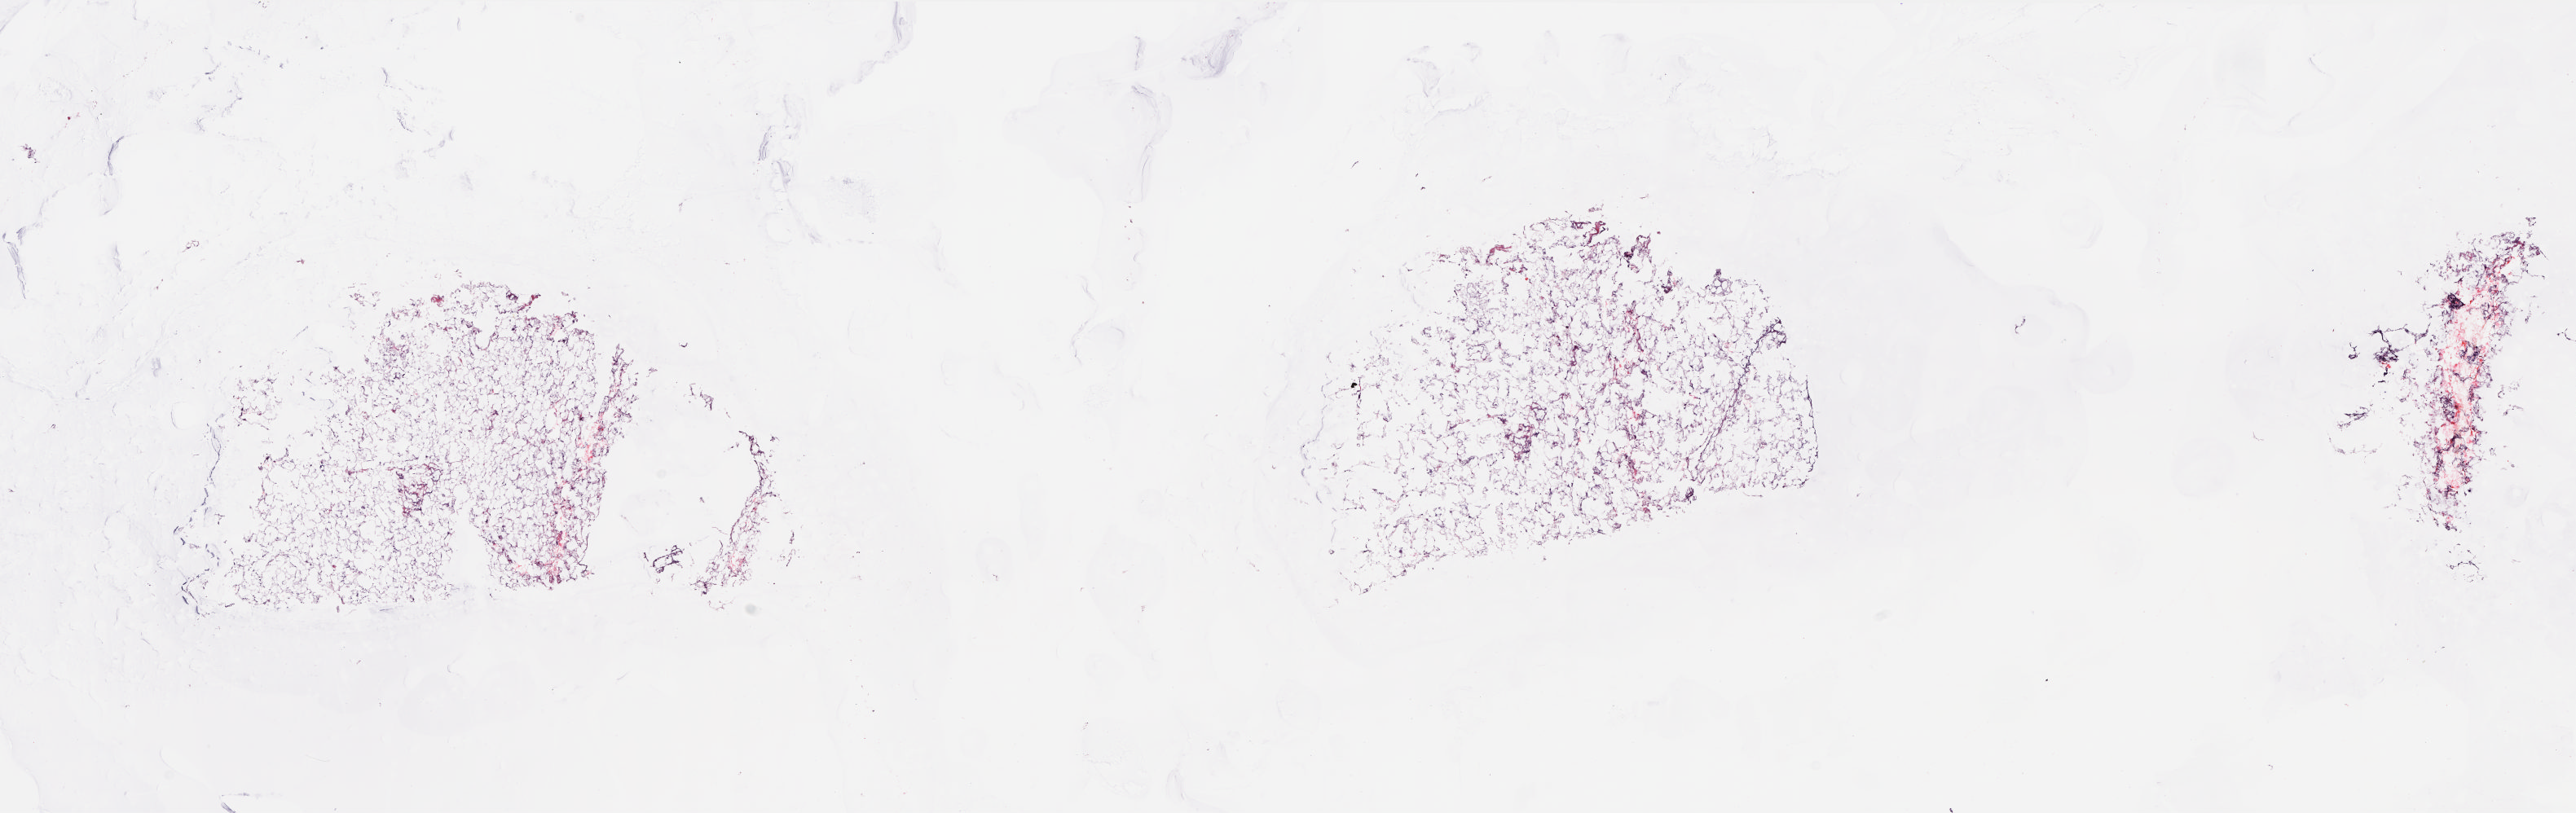
Digitized H&E tissue section (whole slide) — low-resolution overview of the scanned area, about 25.5 x 8.0 mm (from a 20x scan), frozen section, sample: solid tissue normal (non-tumour tissue), connective, subcutaneous and other soft tissues. Male patient; age at initial diagnosis 76 years. Composition of this section per pathologist review: tumour cells 0%, tumour nuclei 0%, normal cells 100%, stromal cells 0%, necrosis 0%. Infiltration values recorded for this section: lymphocyte infiltration 1%, monocyte infiltration 0%, neutrophil infiltration 0%.
This section: solid tissue normal sample (biorepository sample class). Patient diagnosis: Undifferentiated sarcoma (connective, subcutaneous and other soft tissues, NOS).